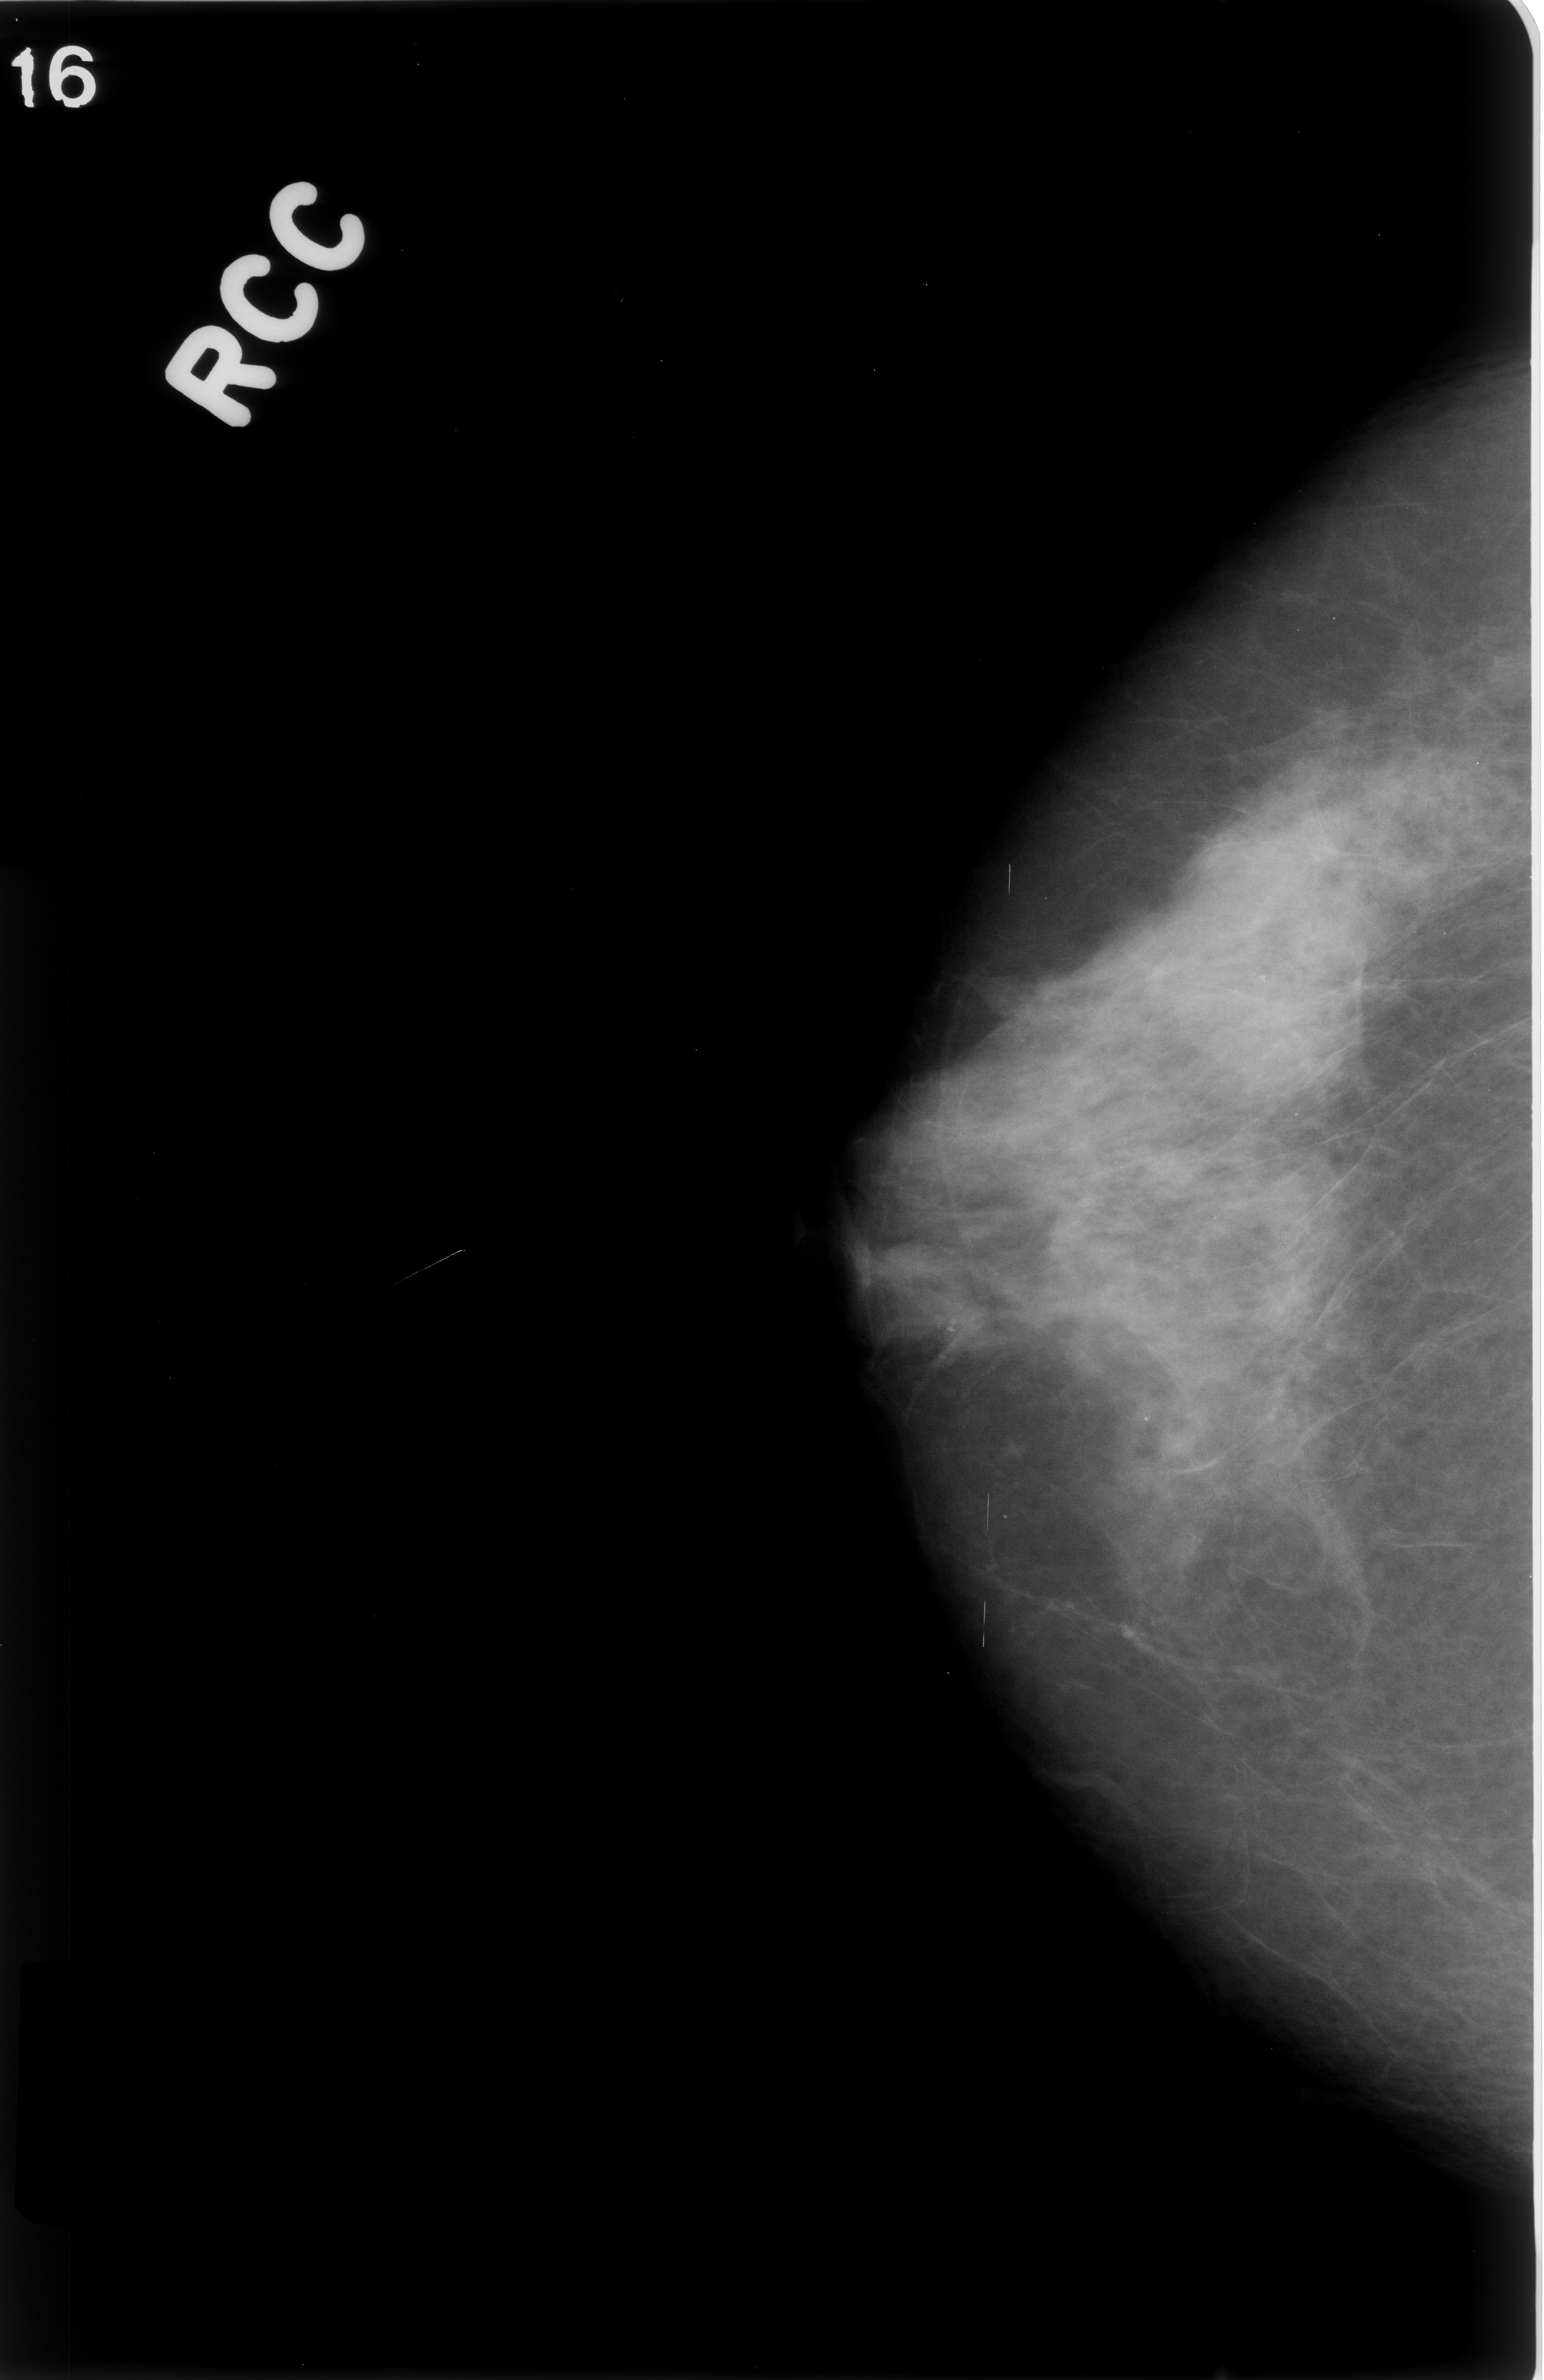
Scanned film-screen mammogram, right breast, craniocaudal (CC) view, BI-RADS breast density category 3 (scale 1–4).
- Abnormality record for this image: Finding 1 of 2: calcifications, morphology amorphous, distribution clustered; BI-RADS assessment category 4; pathology result (as recorded, not read from the image): malignant.
- Finding 2 of 2: calcifications, morphology amorphous, distribution clustered; BI-RADS assessment category 4; subtlety rating 3 on a 1 (subtle) to 5 (obvious) scale; pathology (as recorded): benign.